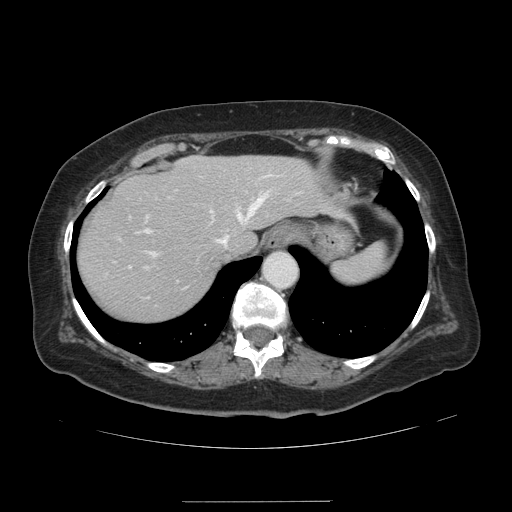
Contrast-enhanced abdominal CT, one axial slice; slice 109 of 141 in the series (ordered by position); 120 kVp; intravenous contrast given; soft-tissue window (W 400 / L 40 HU); 2.5 mm slice thickness; 512 × 512 image matrix, field of view 393 × 393 mm. Female patient, age 74 years. From the clinical record (not read from this slice): diagnosis: colorectal cancer liver metastases, imaged before liver resection; multiple liver metastases: yes; largest metastasis: 7 cm.
Outlined on this slice (manually delineated by an expert):
- hepatic veins: bounding box (x1, y1, x2, y2) in pixels: (146, 190, 270, 258)
- liver: (78, 156, 334, 320)
- planned liver remnant (the part of the liver to remain after resection): (78, 156, 334, 320)
- portal vein (with intrahepatic branches): (128, 202, 256, 267)